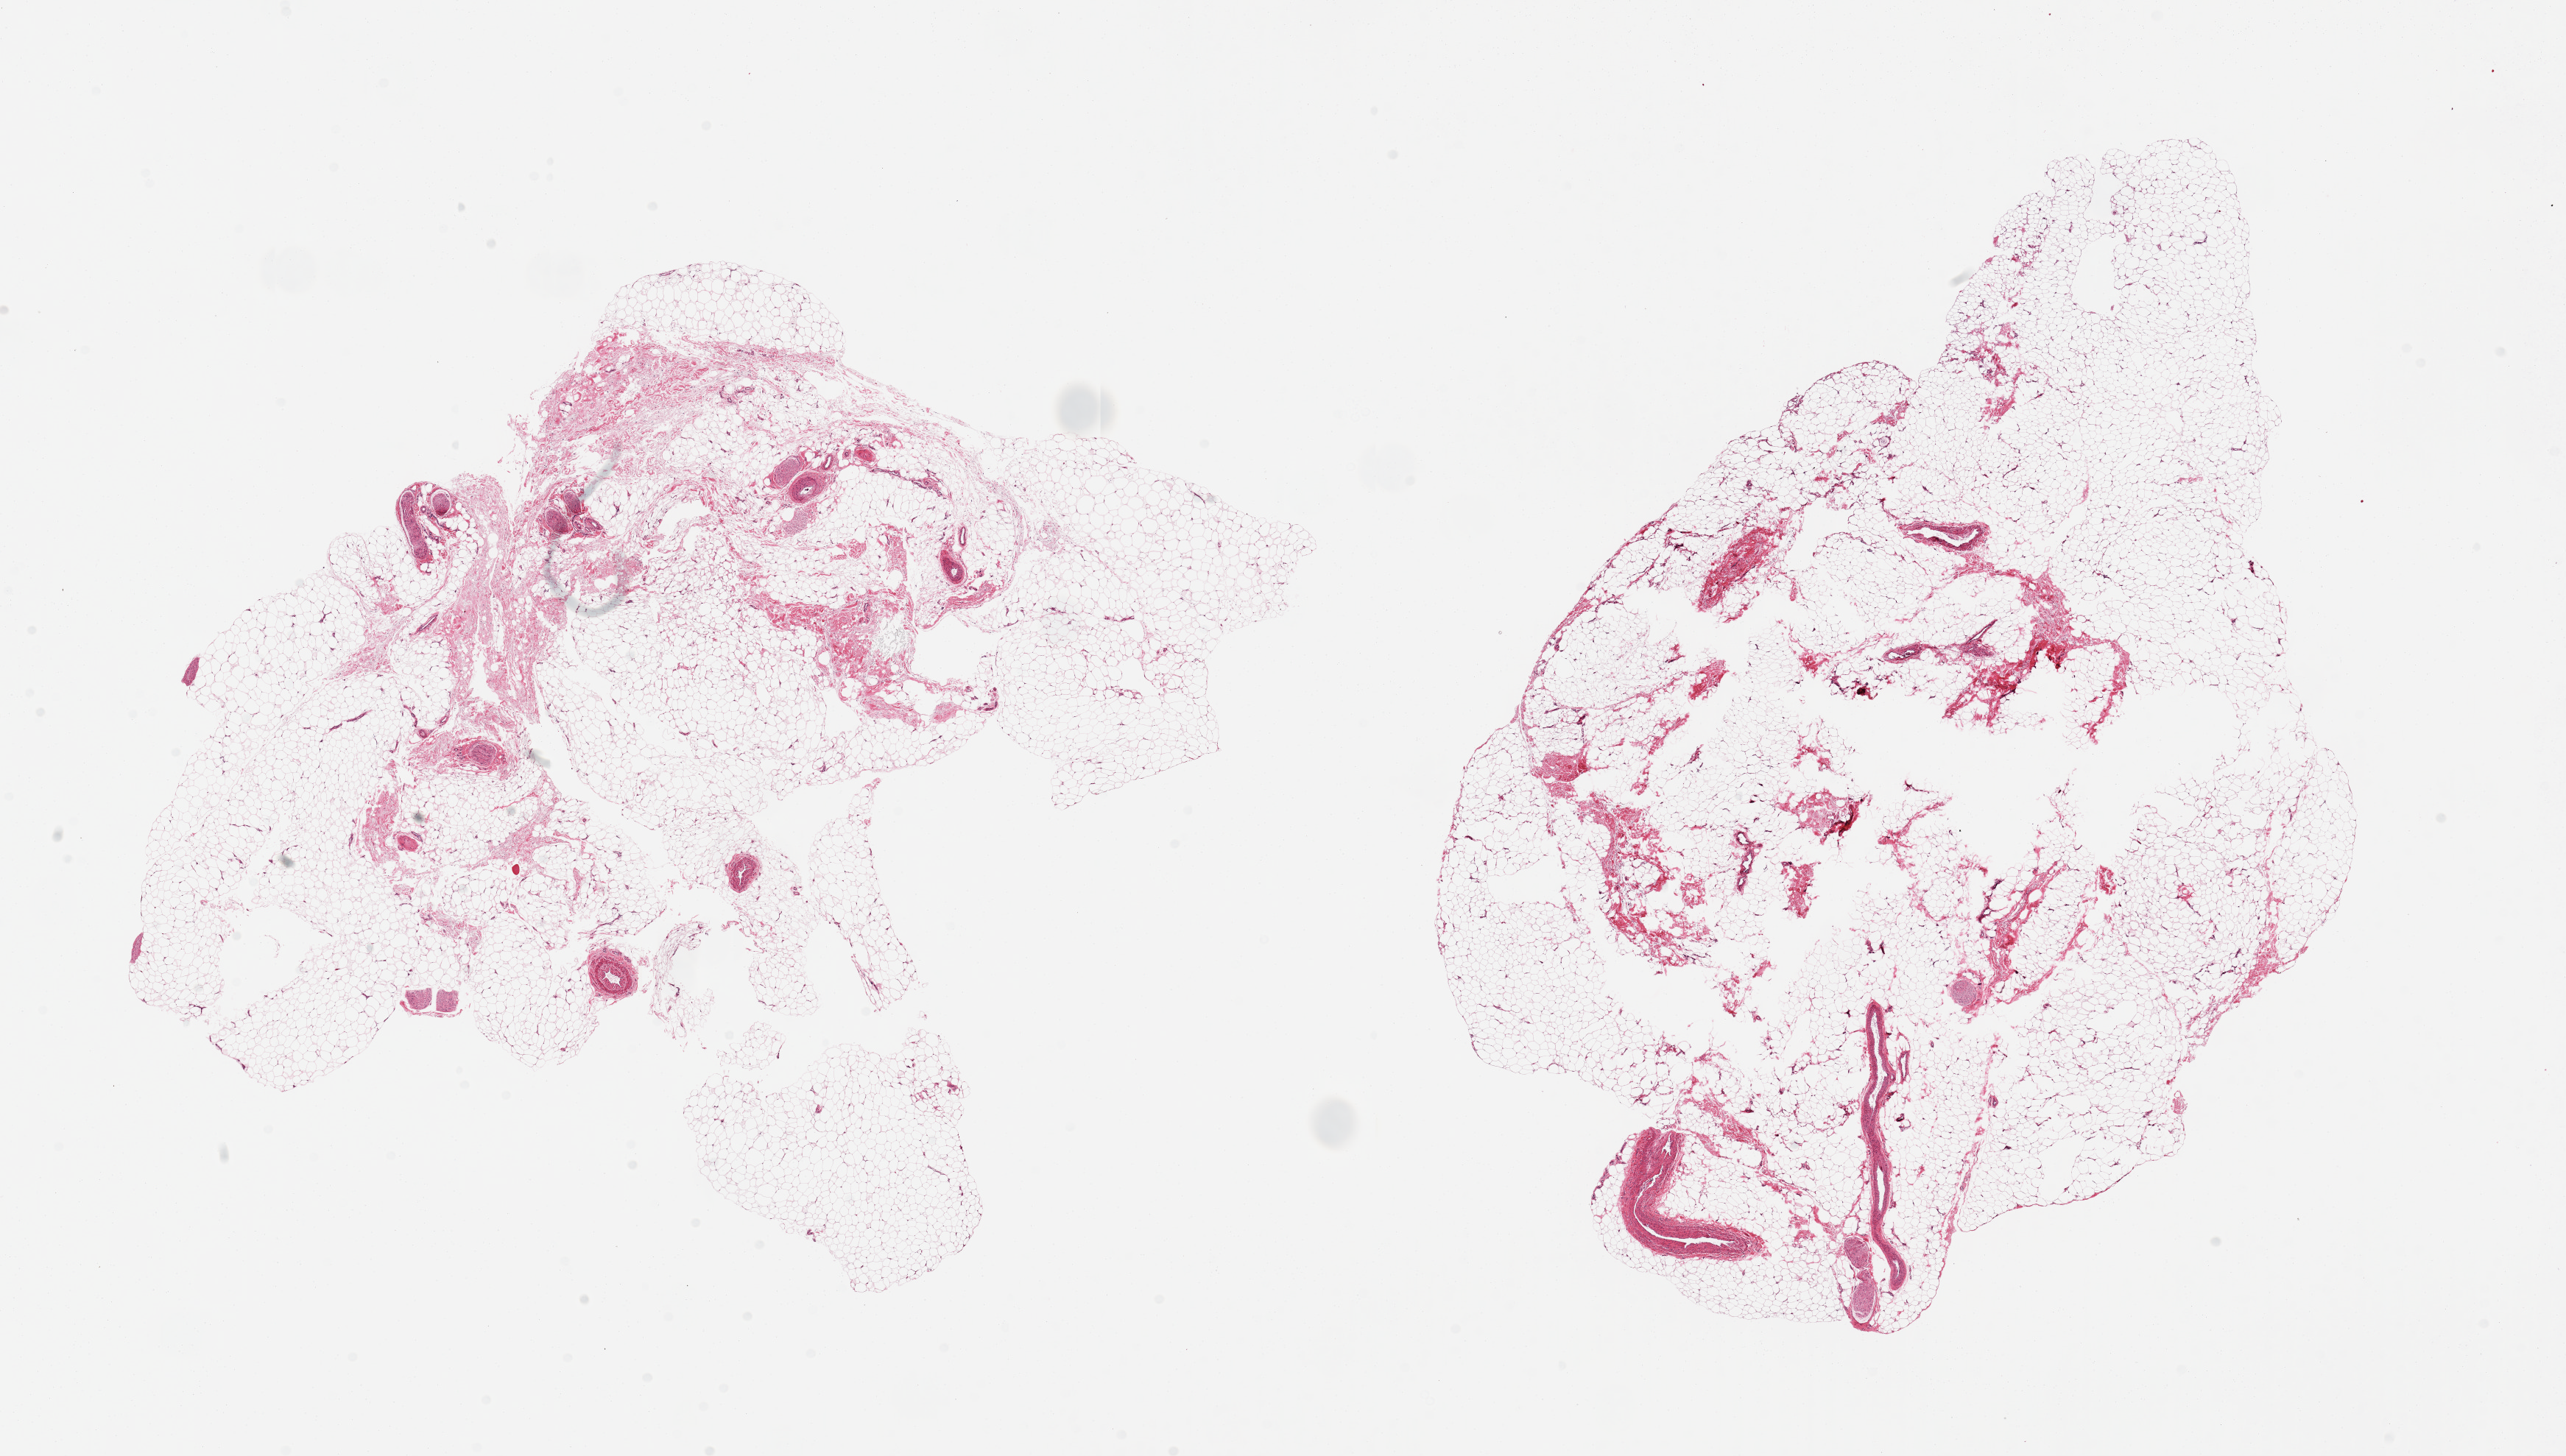
Hematoxylin and eosin (H&E) whole-slide image — shown as a low-resolution overview of the whole scanned area (about 27.6 x 15.6 mm); PAXgene-fixed, paraffin-embedded tissue; section of adipose tissue (target tissue); donor tissue sample. Male donor.
Review note (as recorded): 2 pieces, ~10-15% vascular/fascial tissues.